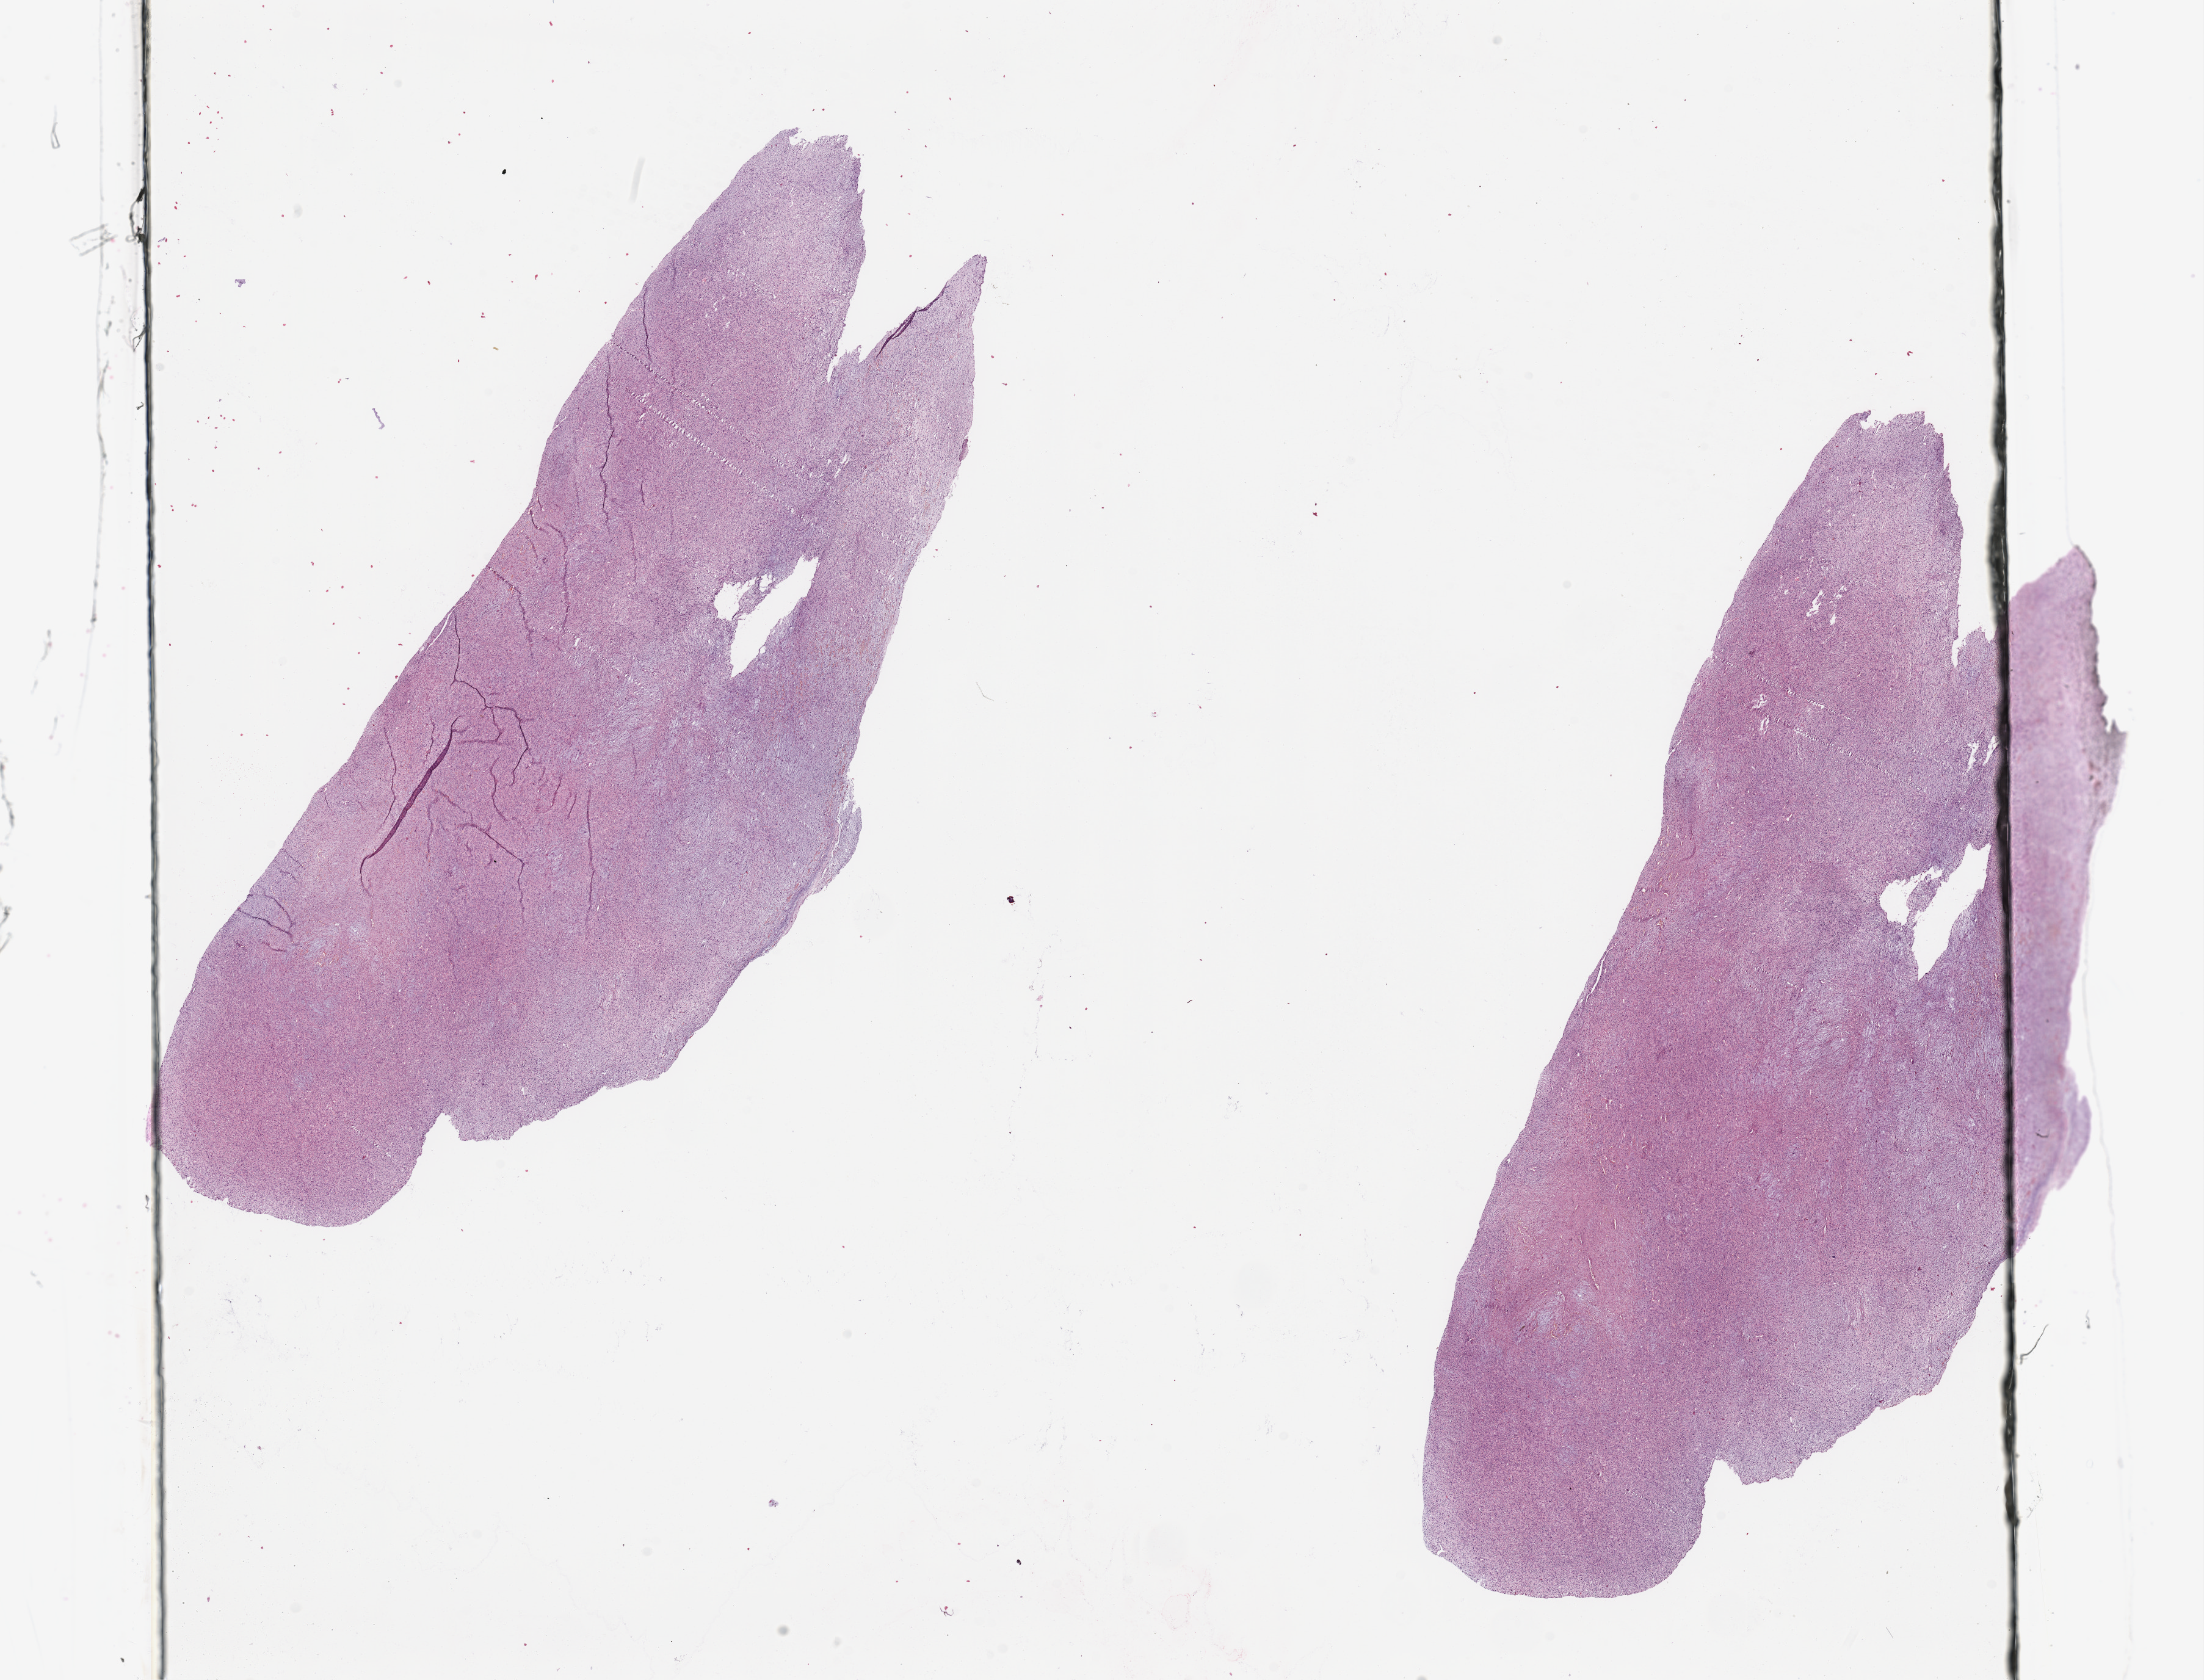
Digitized H&E-stained tissue section (whole slide) — shown as a low-resolution overview of the whole scanned area (about 28.5 x 21.8 mm, slide scanned at 20x). Tumour tissue sample. 72-year-old female patient.
Patient diagnosis (cohort enrolment): sarcoma (site not recorded at cohort level).